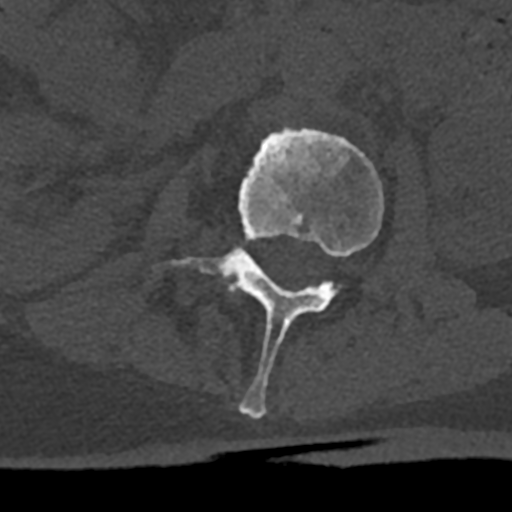
CT including the spine, one axial slice. Position 371 of 797 along the scan axis. Reconstruction kernel Br40s/3. 120 kVp. Bone window (W 1800 / L 400 HU). 512 × 512 image matrix, field of view 160 × 160 mm. Male patient, age 74 years. Case-level facts recorded for this patient, not image findings: primary cancer: renal; vertebrae with lytic lesions (as recorded): T10, L1, L2, L3, L4, L5.
Structures marked on this image (semi-automatically segmented with operator editing):
- L2 vertebra: bounding box <170,128,383,419> (left, top, right, bottom; pixels)
- L3 vertebra: <228,280,245,292>